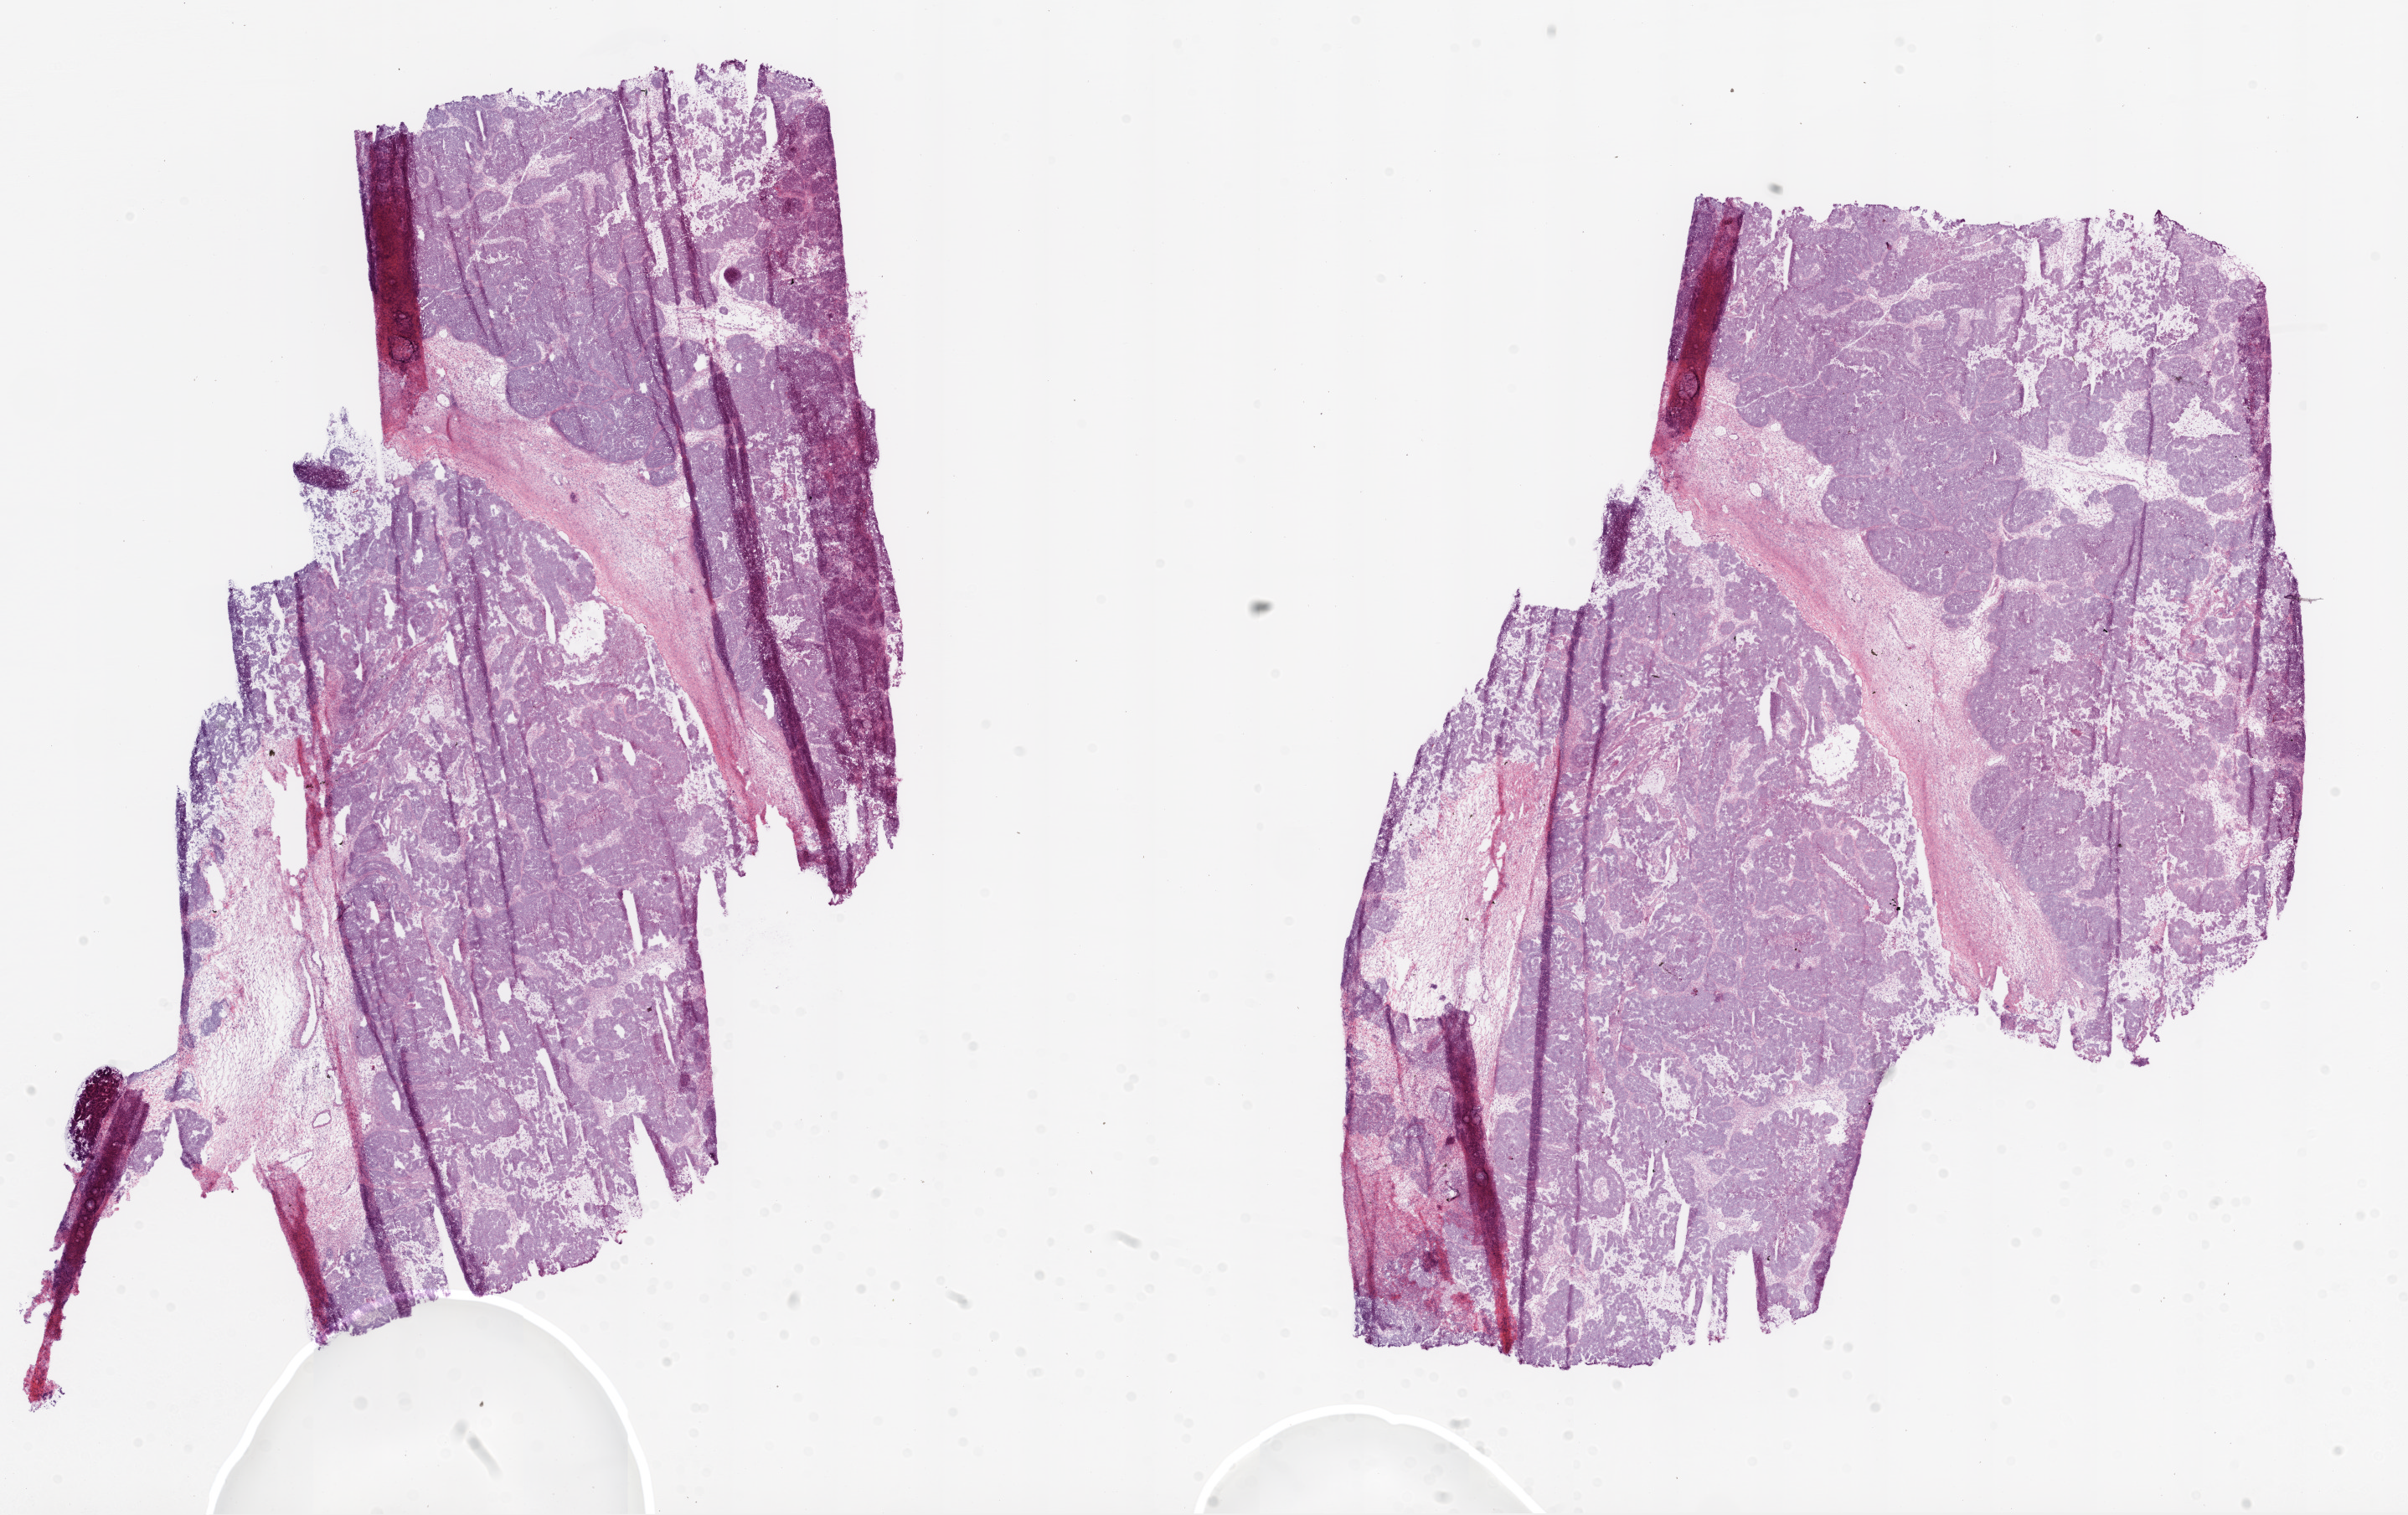
H&E whole-slide image — a low-resolution overview of the entire scanned area, about 23.1 x 14.5 mm (slide scanned at 20x), frozen section, ovary, primary tumour sample. Female, age 40 years at initial diagnosis. Histologic grade: G3 (poorly differentiated). Pathologist review of this section (percent, as recorded): tumour cells 84%, tumour nuclei 90%, normal cells 1%, stromal cells 10%, necrosis 5%.
* diagnosis: Serous cystadenocarcinoma, NOS
* FIGO stage: IIIA